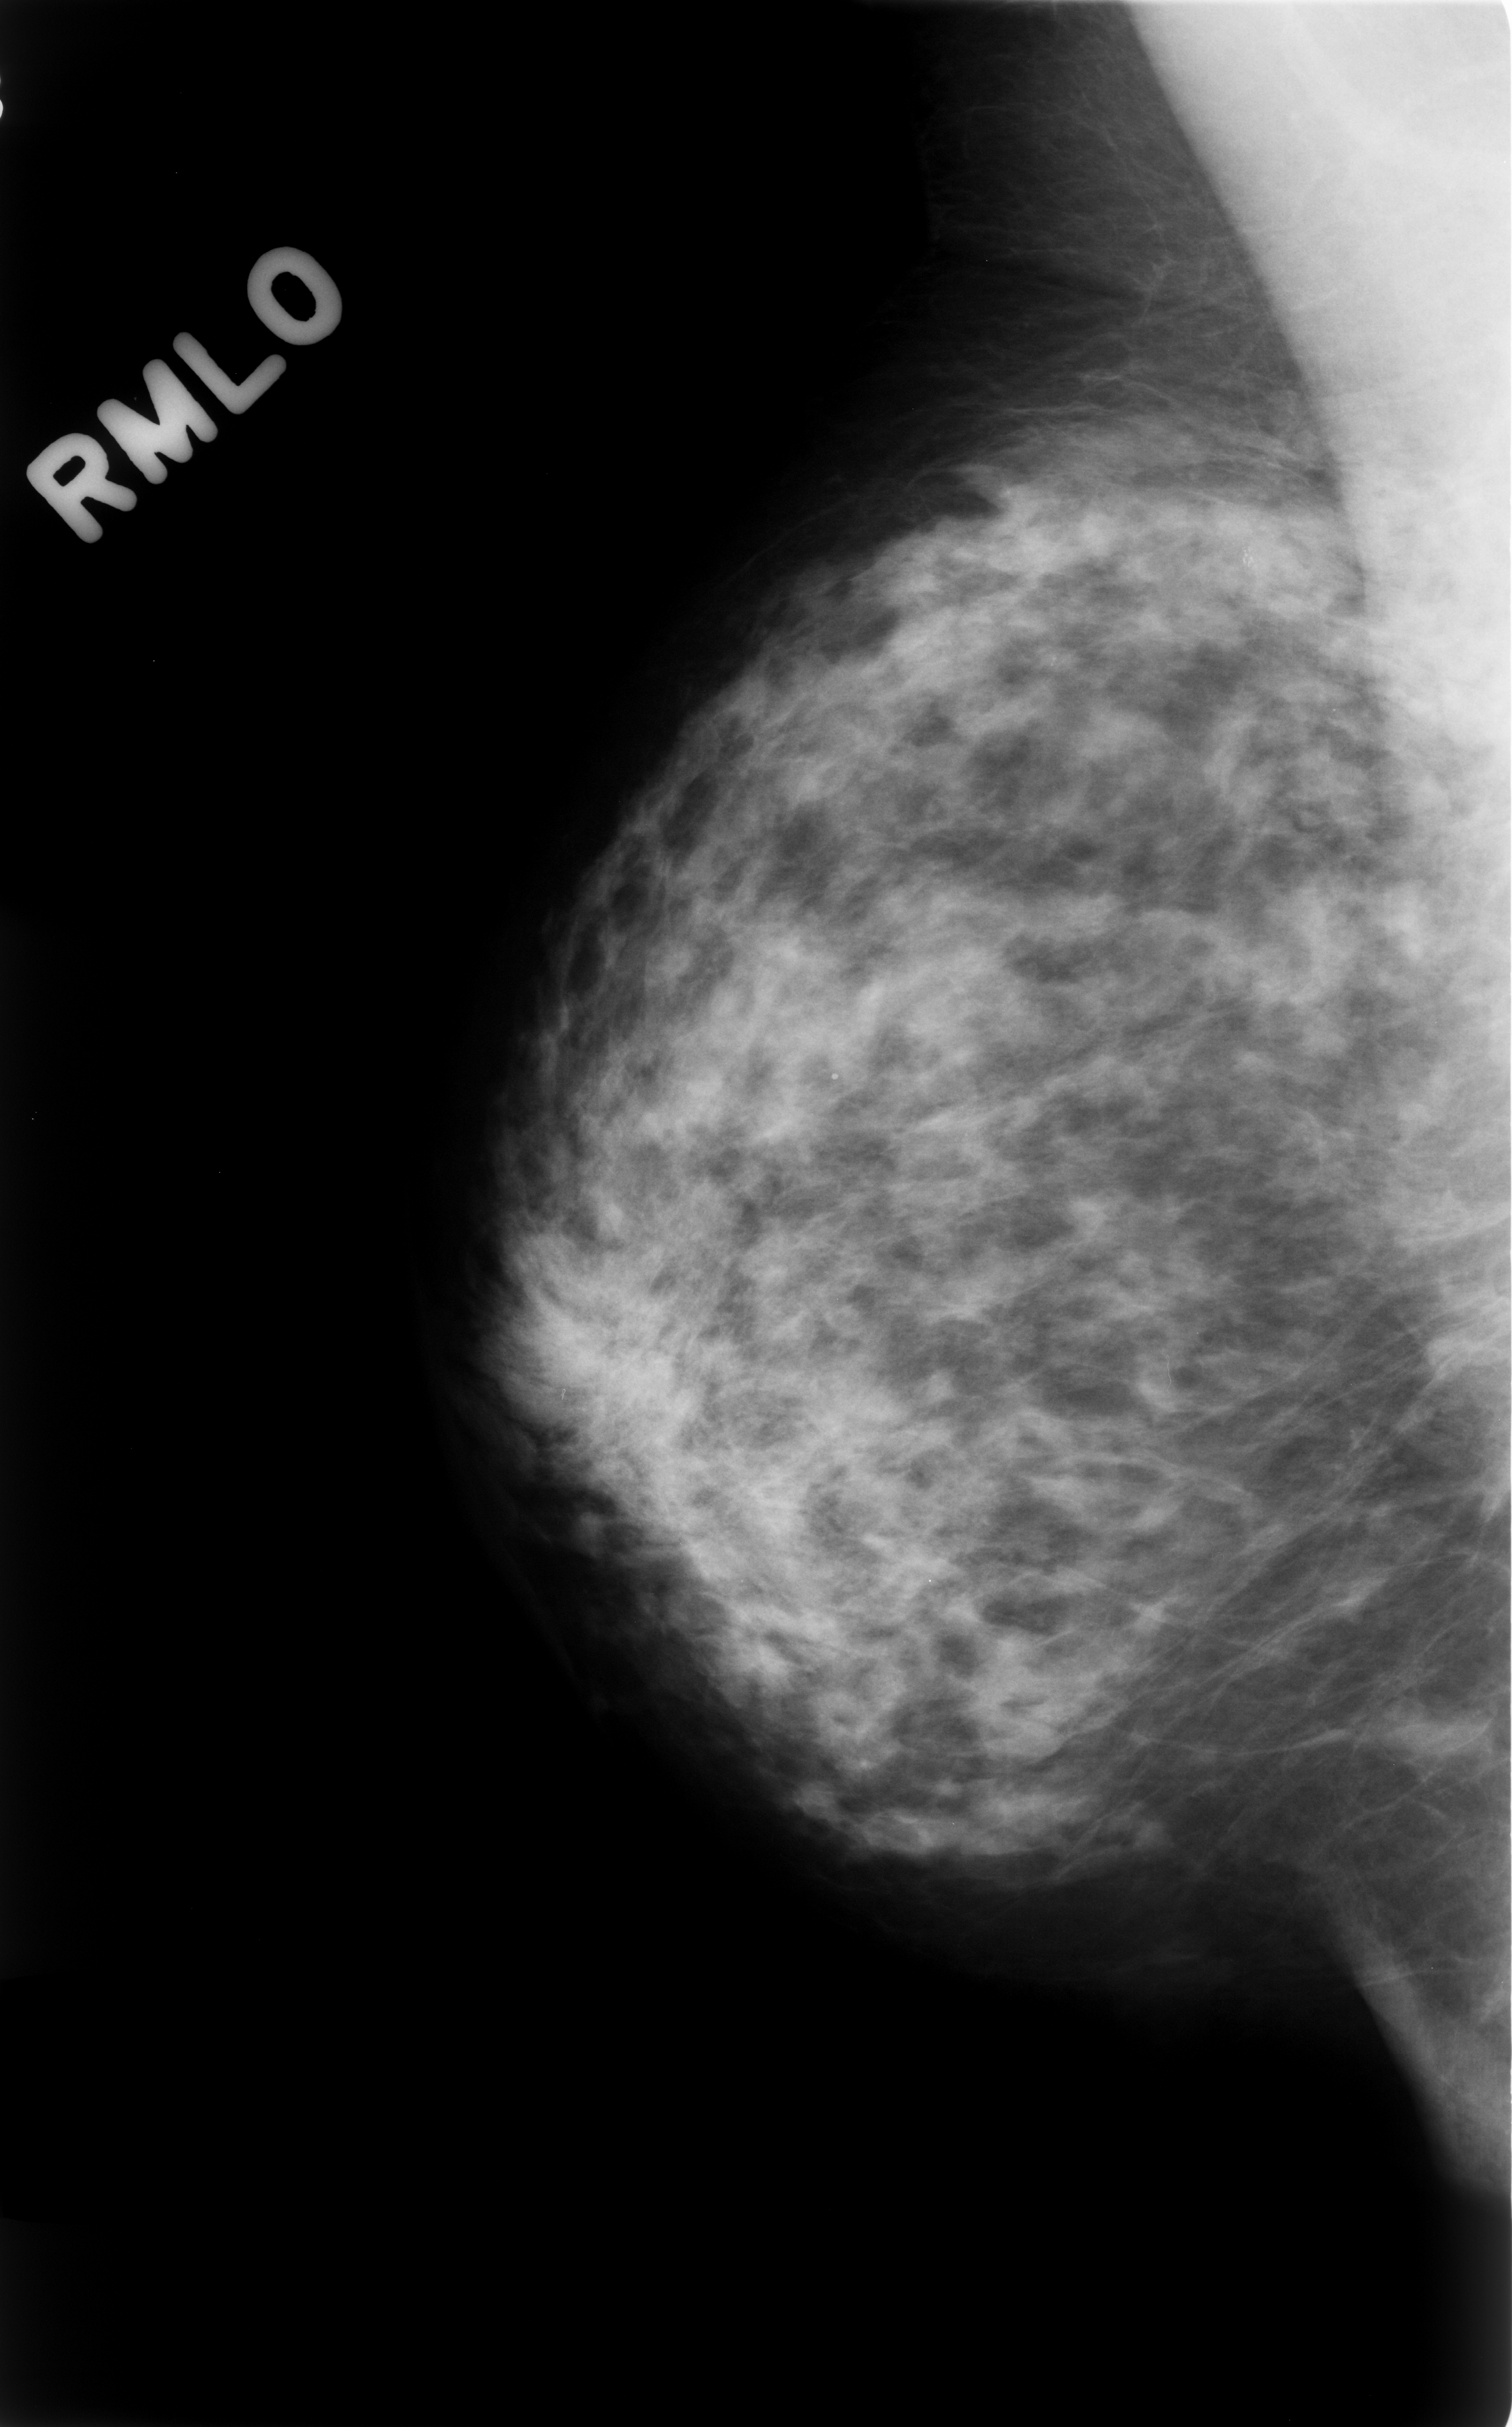
Scanned film-screen mammogram; right breast; MLO view; breast composition: scattered fibroglandular densities (BI-RADS density category 2 of 4).
Abnormality record for this image: calcifications, morphology amorphous, distribution clustered; BI-RADS assessment category 4; pathology (as recorded): benign.